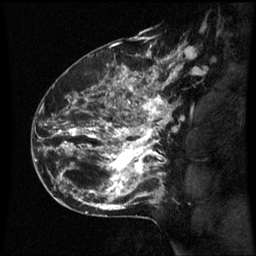
Breast MRI (dynamic contrast-enhanced), one sagittal slice; slice 42 of 60 in the series (ordered by position); dynamic contrast-enhanced series, image 2 of 3 at this slice position (ordered by acquisition); 1.5 T; TE 4.2 ms, TR 8.9 ms; 256 × 256 image matrix, field of view 200 × 200 mm. Female patient, age 42 years. From the clinical record (not read from this slice): setting: breast cancer imaged before/during neoadjuvant chemotherapy; receptor status: HER2-positive.
Structures marked on this image (semi-automatically segmented with operator editing):
- analysis volume of interest (the breast-tissue region the enhancement analysis was run in; not a lesion): bounding box [x1, y1, x2, y2] px = [66, 82, 173, 193]
- tumour enhancement mask (voxels above the 70 % enhancement threshold inside the analysis volume of interest): [66, 82, 171, 193]